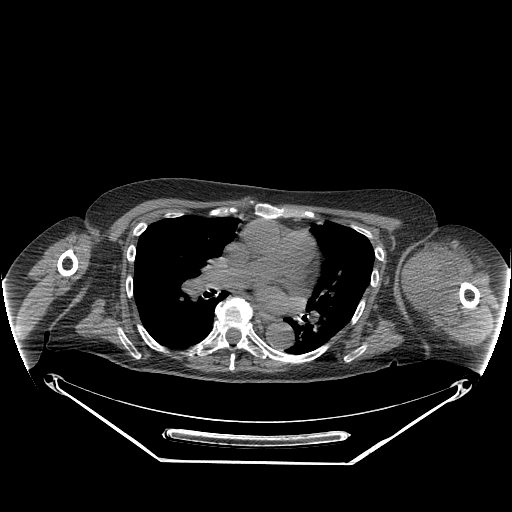
CT of an extremity soft-tissue mass (from a PET/CT study), one axial slice; position 177 of 267 along the scan axis; reconstruction kernel STANDARD; 140 kVp; soft-tissue window (W 400 / L 40 HU); 512 × 512 image matrix. Female patient. From the clinical record (not read from this slice): histological type: pleiomorphic leiomyosarcoma; grade: high; site of the primary tumour: left biceps.
Structures marked on this image (expert contour drawn on MRI and transferred to this co-registered scan by the dataset authors):
- gross tumour volume including surrounding oedema: bounding box (x1, y1, x2, y2) in pixels: (406, 244, 465, 325)
- gross tumour volume (mass): (406, 244, 462, 309)